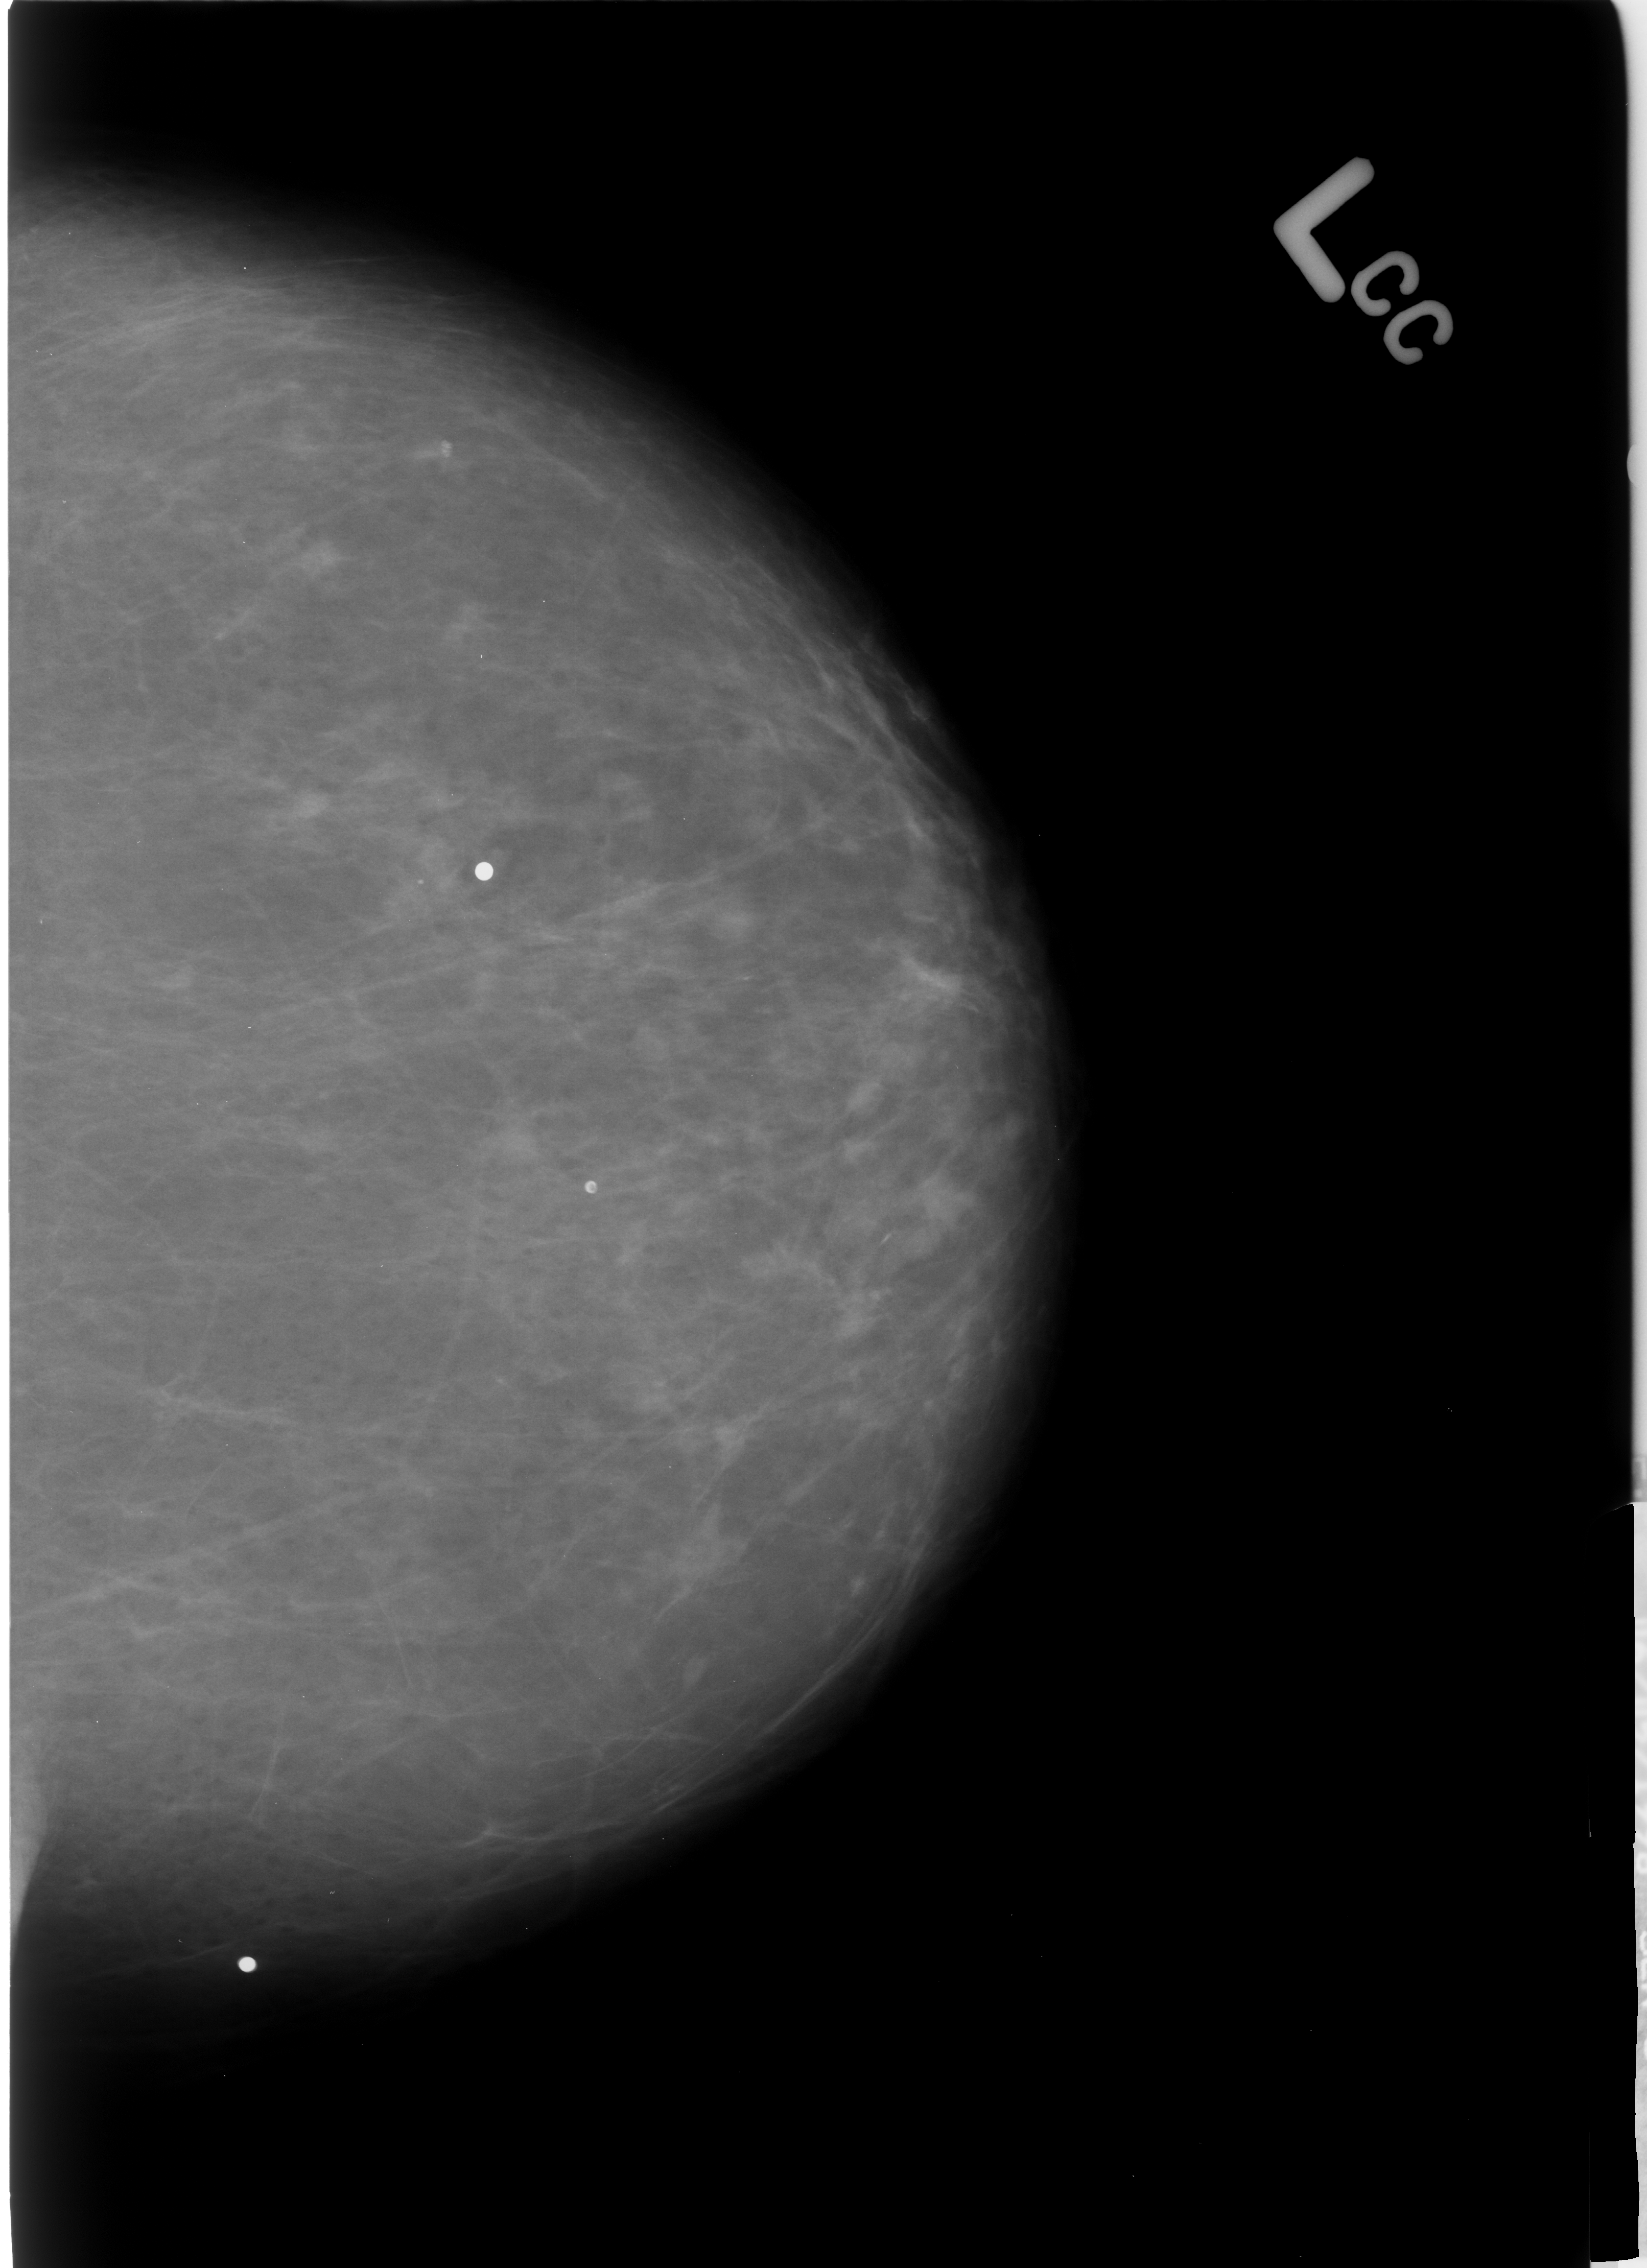
Scanned film-screen mammogram; left breast; CC view; breast composition: almost entirely fatty (BI-RADS density category 1 of 4); 1647 × 2268 image matrix.
Expert-marked regions of interest on this image (one box per marked abnormality):
- calcifications, morphology lucent center; BI-RADS assessment category 2; benign; no additional work-up was recommended (outcome (as recorded, no biopsy): benign without callback): box from (x=576, y=1168) to (x=606, y=1207) px